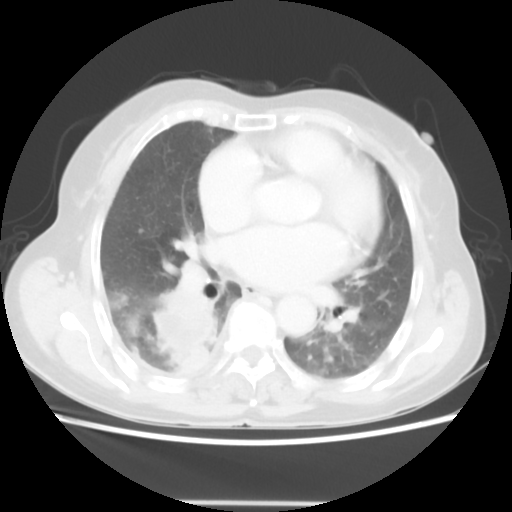
Chest CT, one axial slice. Position 25 of 52 along the scan axis. 140 kVp. Lung window (W 1500 / L -600 HU). 5 mm slice thickness. 512 × 512 image matrix, field of view 337 × 337 mm. Patient: female, 67 years. Case-level facts recorded for this patient, not image findings: clinical TNM (as recorded): T3 N1 M1.
Structures marked on this image (rectangle marked by the reading radiologist):
- lung tumour (recorded histology: adenocarcinoma): bounding box (x1, y1, x2, y2) in pixels: (151, 287, 217, 371)